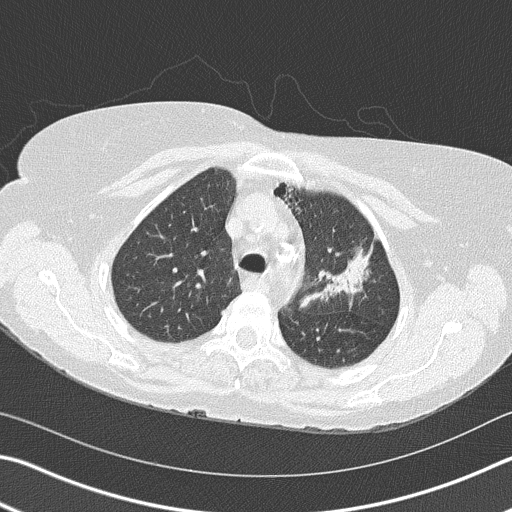
Axial slice from a low-dose chest CT screening exam. Second annual screen. Lung window (W 1500 / L -600 HU). 2 mm slice thickness. 120 kVp. Slice 122 of 153 in the series. 512 × 512 image matrix. Female, age 68 years at enrolment. Former smoker at enrolment.
• Lesion marked by an expert reader, bounding box (x1, y1, x2, y2) in pixels: (292, 216, 383, 318).
• The exam's reader record, not a measurement of the box and not confirmed to be the same lesion: non-calcified nodule or mass ≥4 mm, left upper lobe, 4 × 2 mm, spiculated (stellate) margins, soft tissue attenuation, pre-existing on the prior screen: yes; interval growth: yes.
• Lung cancer was diagnosed 392 days after this screen (after the third annual screen): adenocarcinoma, NOS, left upper lobe, poorly differentiated (G3), stage IB (AJCC 6th edition), 50 mm at pathology.